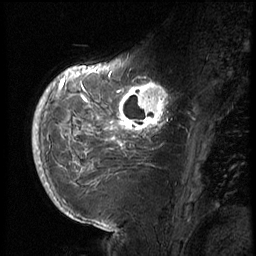
Breast MRI (dynamic contrast-enhanced), one sagittal slice. Position 22 of 72 along the scan axis. 3 images stored at this slice position (order not interpretable as contrast timing). 1.5 T. TE 4.2 ms, TR 8.9 ms. 2.5 mm slice thickness. 256 × 256 image matrix, field of view 200 × 200 mm. Female patient, age 56 years. Case-level facts recorded for this patient, not image findings: setting: breast cancer imaged before/during neoadjuvant chemotherapy.
Outlined on this slice (semi-automatic segmentation, software-assisted and operator-edited):
- analysis volume of interest (the breast-tissue region the enhancement analysis was run in; not a lesion): box from (x=114, y=76) to (x=177, y=138) px
- tumour enhancement mask (voxels above the 140 % enhancement threshold inside the analysis volume of interest): (x=117, y=77)–(x=169, y=131)